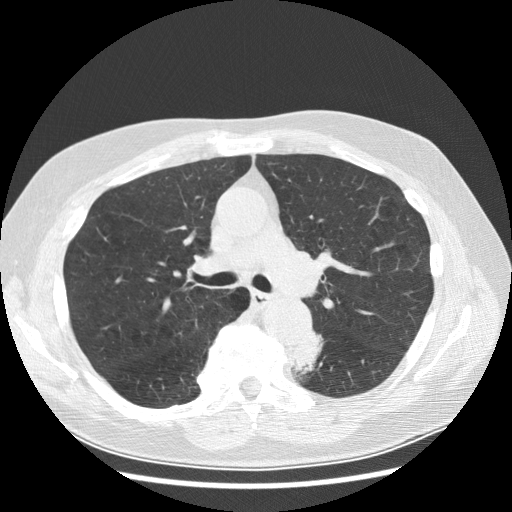
Low-dose screening chest CT, axial slice. Baseline screening round. Lung window (W 1500 / L -600 HU). Slice 101 of 282 in the series. Male participant, aged 70 years at enrolment. Current smoker at enrolment.
Expert-annotated lung lesion, bounding box (x1, y1, x2, y2) in pixels: (278, 332, 328, 381). Reader record for this screening exam (exam-level; its link to the box is not recorded): non-calcified nodule or mass ≥4 mm, left lower lobe, 27 × 16 mm, spiculated (stellate) margins, soft tissue attenuation, pre-existing on the prior screen: yes; interval growth: yes. Official screen result: positive, change unspecified: nodule(s) >= 4 mm or enlarging nodule(s), mass(es), or other non-specific abnormalities suspicious for lung cancer. Lung cancer was diagnosed 97 days after this screen: papillary adenocarcinoma, NOS, left lower lobe, moderately differentiated (G2), stage IB (AJCC 6th edition), 35 mm at pathology.